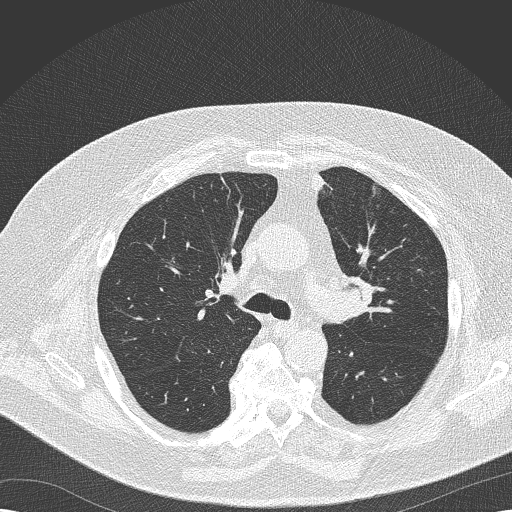
Axial slice from a low-dose chest CT screening exam, second annual screen, lung window (W 1500 / L -600 HU), 2 mm slice thickness. Male participant, aged 68 years at enrolment. Former smoker at enrolment.
Expert reader's lesion annotation, bounding box <322,268,374,332> (left, top, right, bottom; pixels). The exam's reader record, not a measurement of the box and not confirmed to be the same lesion: non-calcified nodule or mass ≥4 mm, left lower lobe, 8 × 6 mm, soft tissue attenuation, pre-existing on the prior screen: yes; interval growth: no. Official screen result: positive, no significant change: stable abnormalities potentially related to lung cancer, unchanged since the prior screening exam. Participant outcome: lung cancer diagnosed 256 days after this screen — squamous cell carcinoma, NOS, left upper lobe, poorly differentiated (G3), stage IIB (AJCC 6th edition), 35 mm at pathology.